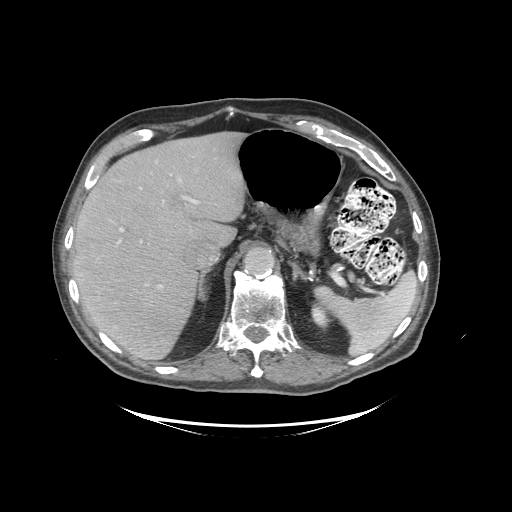
Contrast-enhanced abdominal CT (liver protocol), one axial slice. Slice 69 of 99 in the series (ordered by position). Reconstruction kernel STANDARD. Soft-tissue window (W 400 / L 40 HU). 2.5 mm slice thickness. 512 × 512 image matrix, field of view 460 × 460 mm. Case-level facts recorded for this patient, not image findings: diagnosis: hepatocellular carcinoma (patient treated with transarterial chemoembolisation; whether this scan precedes or follows treatment is not stated here); TNM stage (as recorded): Stage-I; Child-Pugh class: A; tumour differentiation: moderately differentiated.
Structures marked on this image (semi-automatic segmentation, software-assisted and operator-edited):
- liver parenchyma outside the tumour (the mass and vessels are separate outlines, so this box may not span the whole liver): bounding box [x1, y1, x2, y2] px = [72, 132, 246, 358]
- liver vessels: [117, 179, 198, 288]